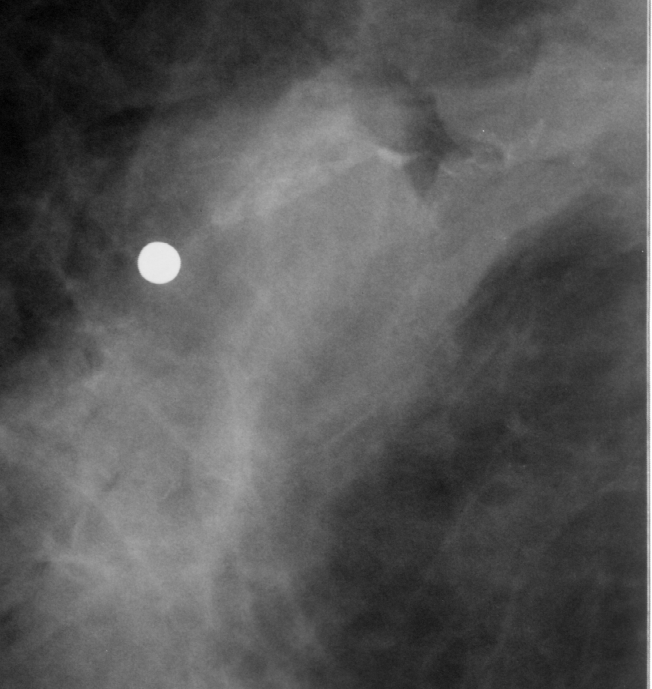
Cropped region of a digitized screen-film mammogram centred on a radiologist-marked abnormality; right breast; CC view; BI-RADS breast density category 2 (scale 1–4).
Finding: calcifications, morphology fine linear branching, distribution linear; BI-RADS assessment category 4; pathology (as recorded): malignant.